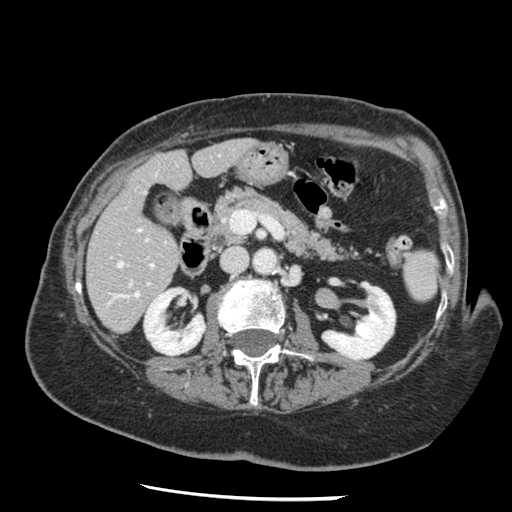
Contrast-enhanced abdominal CT, one axial slice. Position 59 of 148 along the scan axis. Reconstruction kernel STANDARD. Intravenous contrast given. Soft-tissue window (W 400 / L 40 HU). 2.5 mm slice thickness. 512 × 512 image matrix, field of view 330 × 330 mm. Female patient, age 85 years. Case-level facts recorded for this patient, not image findings: diagnosis: colorectal cancer liver metastases, imaged before liver resection; multiple liver metastases: no; largest metastasis: 0.9 cm; disease in both lobes: no.
Annotated regions visible in this slice (expert manual segmentation):
- hepatic veins: bounding box <115,229,142,297> (left, top, right, bottom; pixels)
- liver: <88,139,252,333>
- planned liver remnant (the part of the liver to remain after resection): <88,139,252,333>
- portal vein (with intrahepatic branches): <150,264,153,267>